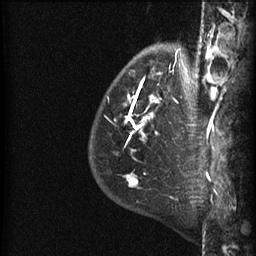
Breast MRI (dynamic contrast-enhanced), one sagittal slice; position 10 of 60 along the scan axis; dynamic contrast-enhanced series, image 2 of 3 at this slice position (ordered by acquisition); 1.5 T; TE 4.2 ms, TR 22.7 ms; 1.5 mm slice thickness; 256 × 256 image matrix, field of view 180 × 180 mm. Female patient, age 48 years. From the clinical record (not read from this slice): setting: breast cancer imaged before/during neoadjuvant chemotherapy; receptor status: triple-negative.
Outlined on this slice (semi-automatic segmentation, software-assisted and operator-edited):
- analysis volume of interest (the breast-tissue region the enhancement analysis was run in; not a lesion): bounding box (x1, y1, x2, y2) in pixels: (89, 43, 191, 180)
- tumour enhancement mask (voxels above the 90 % enhancement threshold inside the analysis volume of interest): (126, 68, 175, 180)